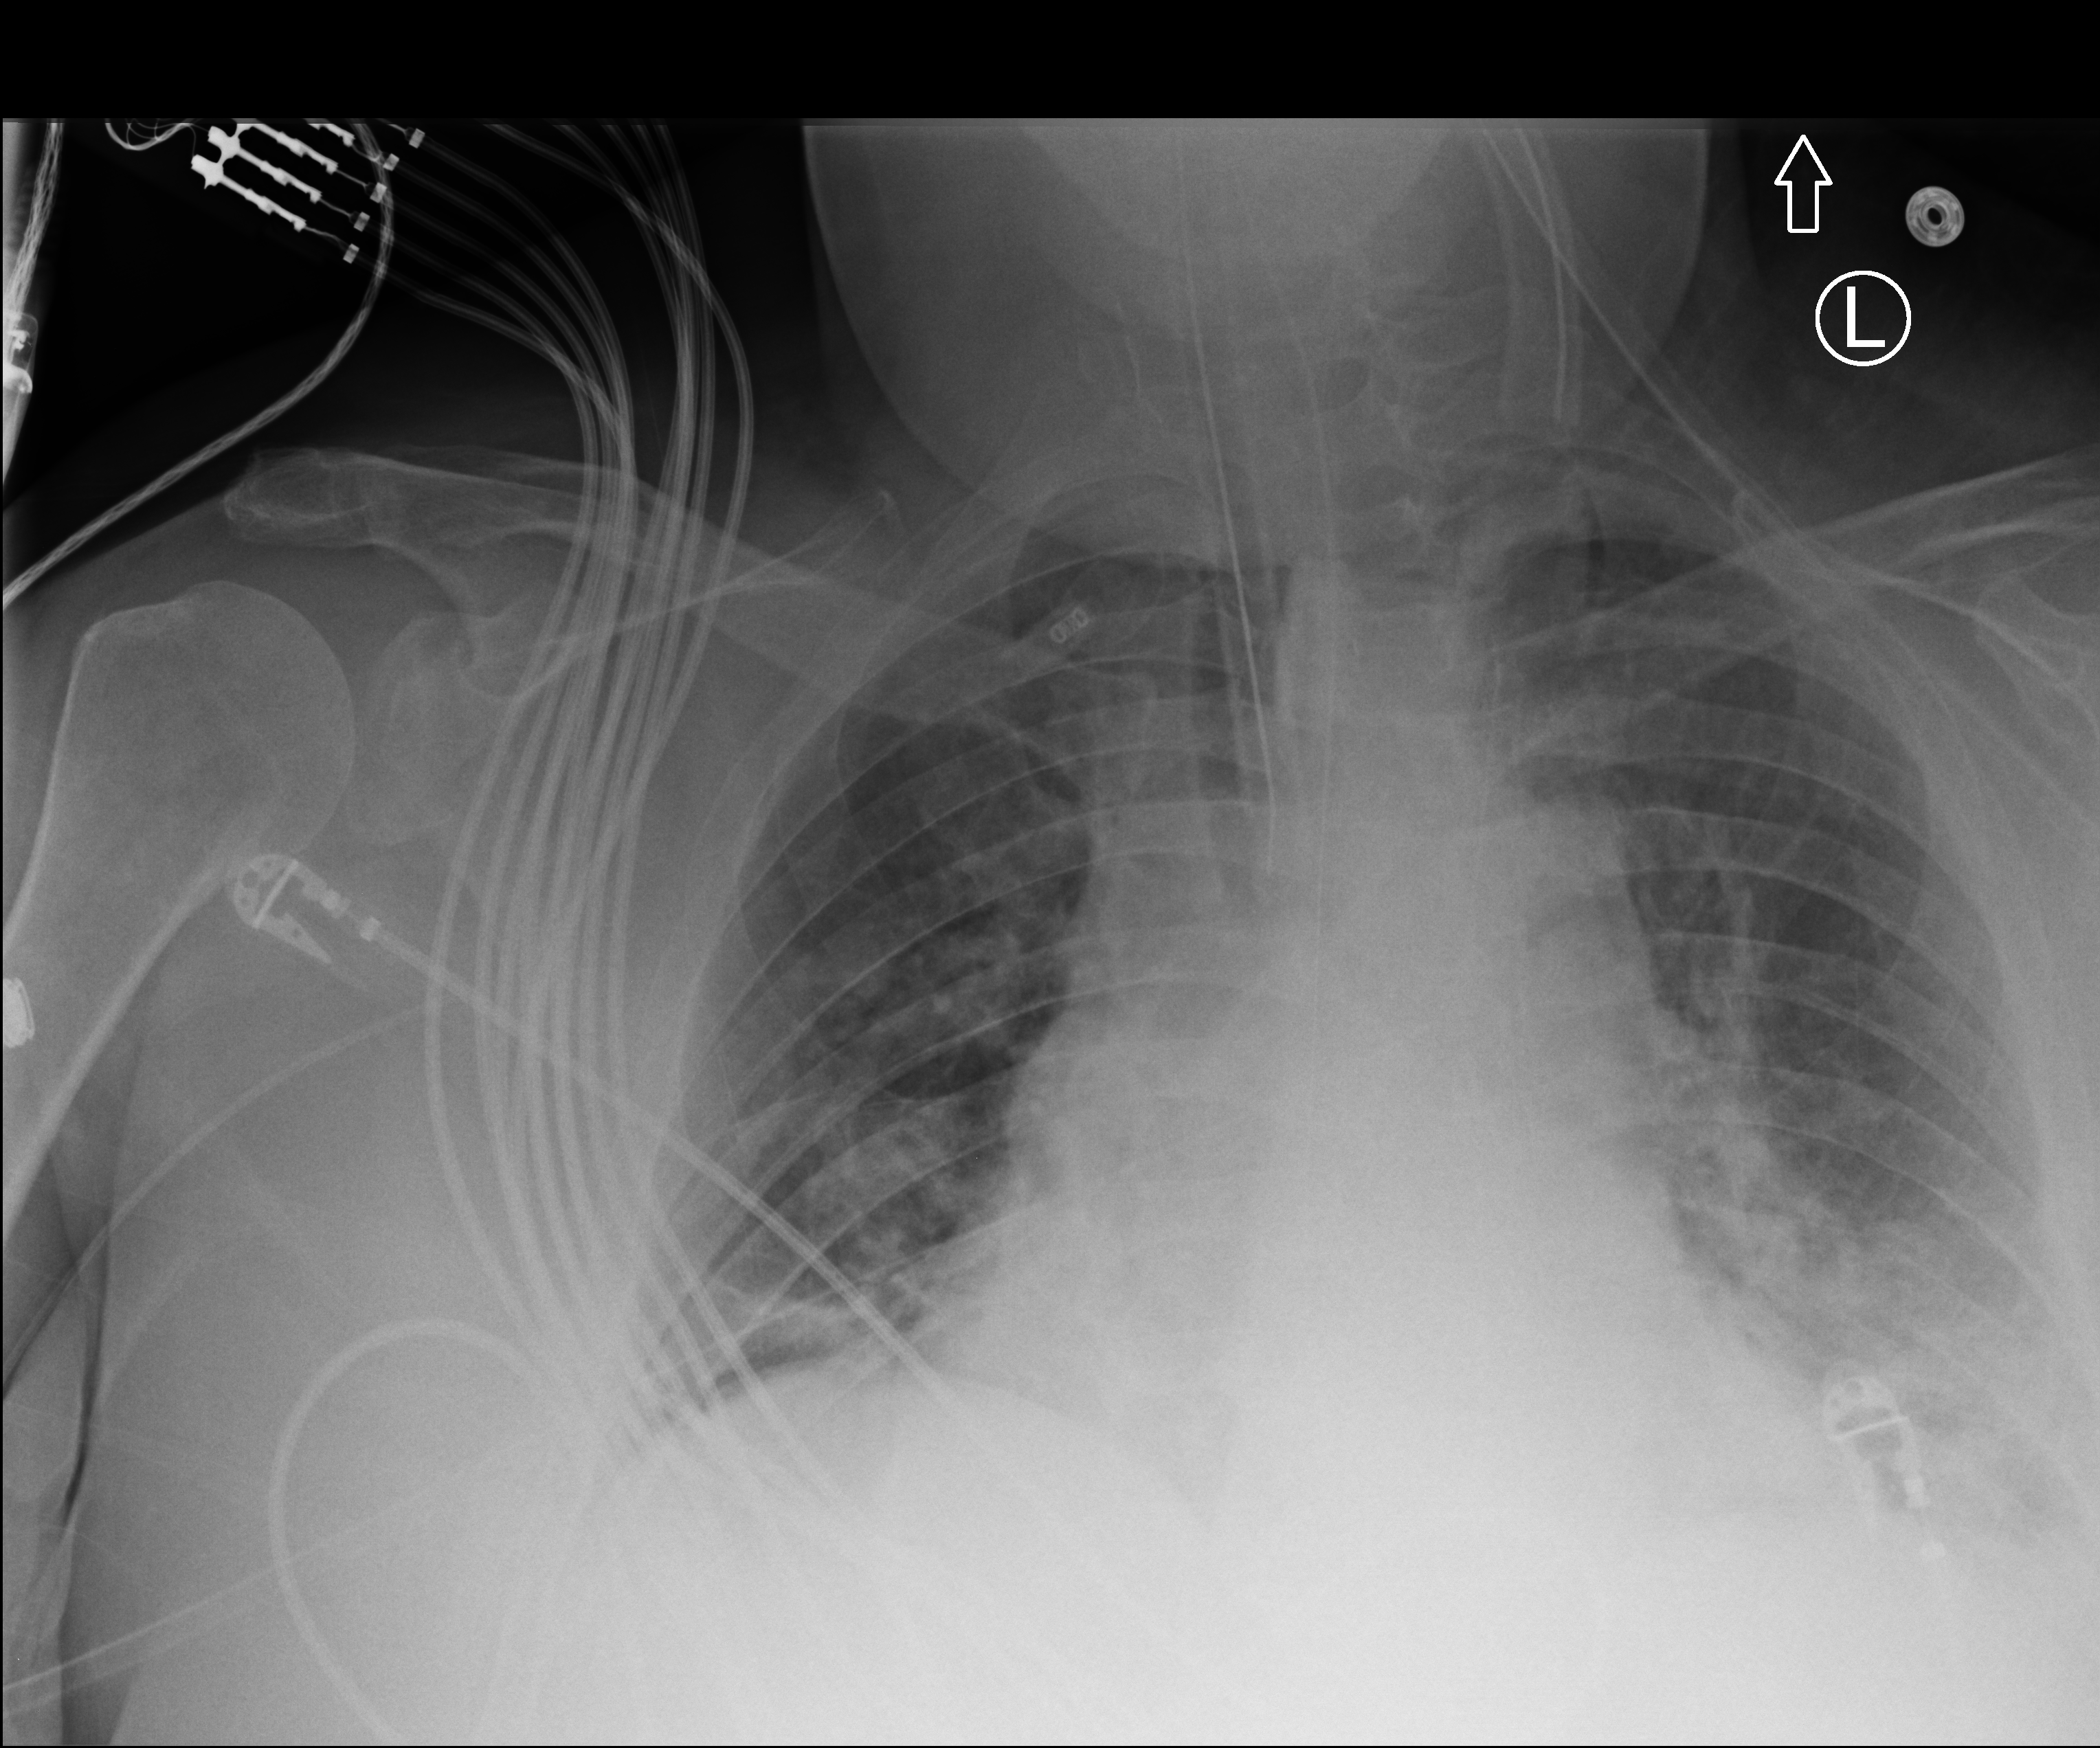
Chest X-ray (portable); anteroposterior (AP) projection. Male patient hospitalised with COVID-19, age 60–74 years.
Hospital-stay facts (about this admission, not read from this image; timing relative to this image not recorded): mechanically ventilated during this hospital stay: yes.